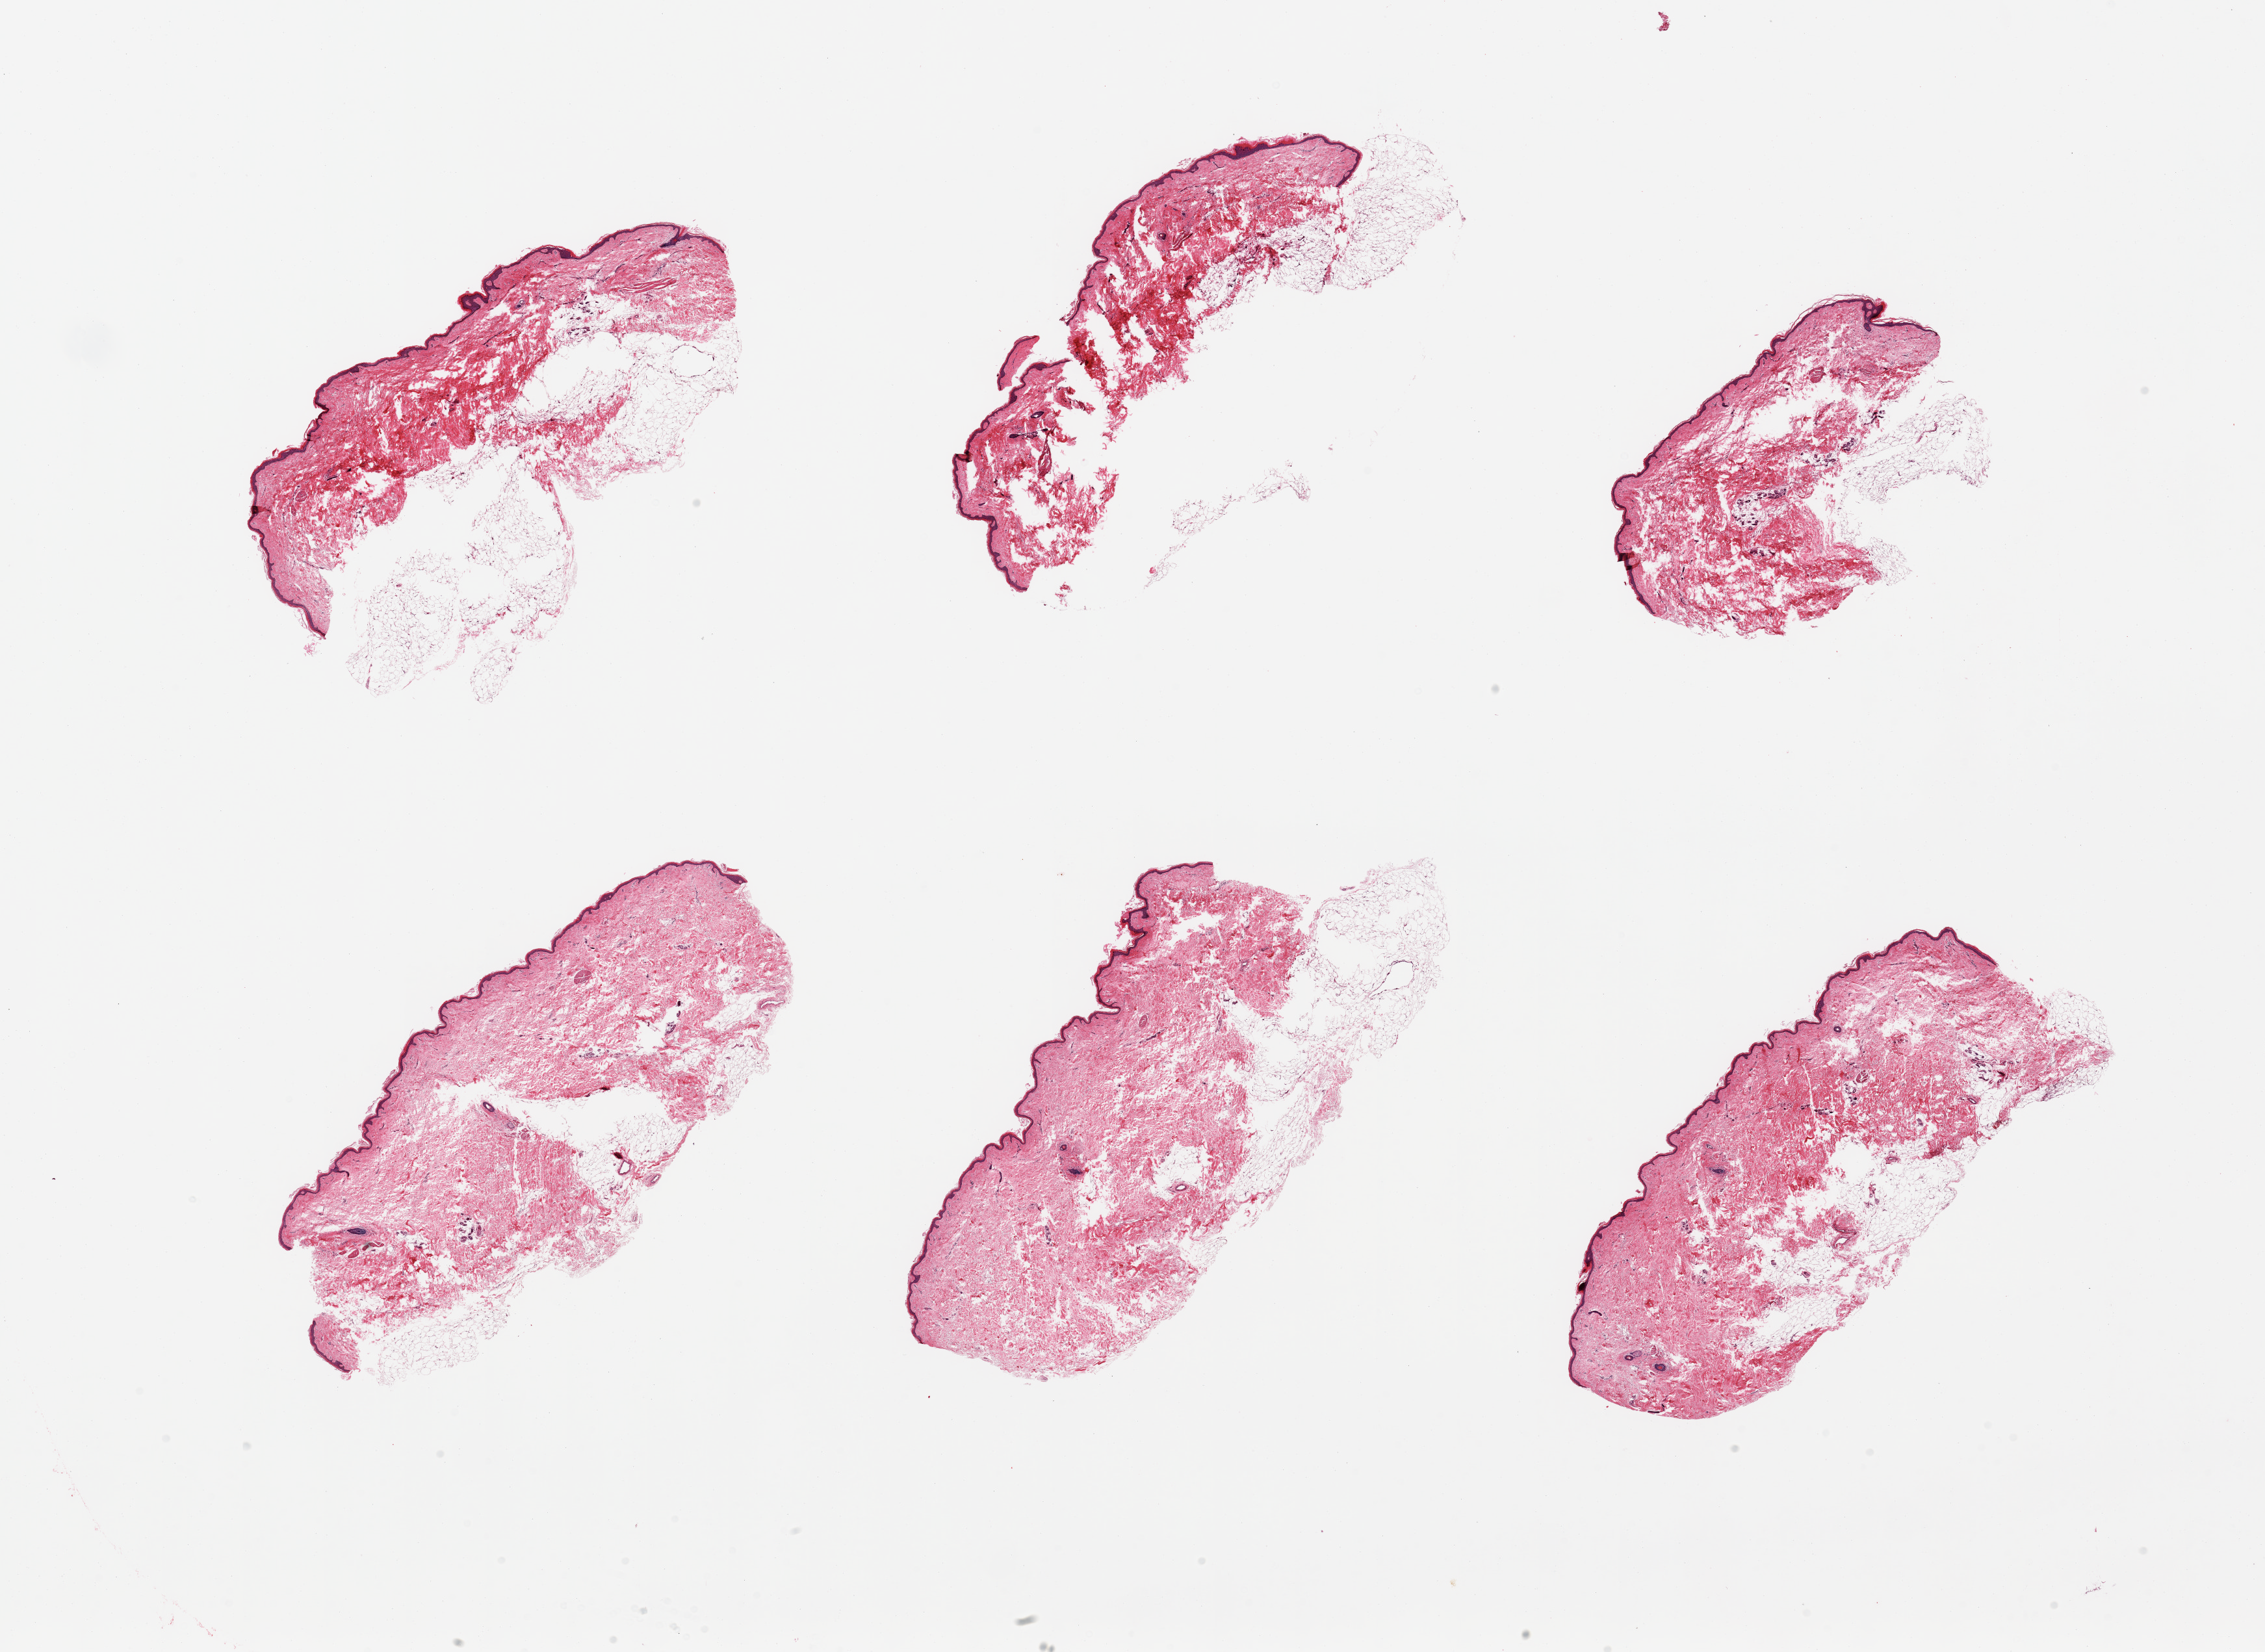
Digitized hematoxylin and eosin (H&E)-stained section, whole scanned area (about 27.6 x 20.1 mm, acquisition: 20x scan) shown as a low-resolution overview. PAXgene-fixed paraffin-embedded (PFPE) section. Sampled site (target tissue): skin of suprapubic region. Donor tissue sample. Donor: female.
Reviewer comment on this tissue sample: 6 pieces, adherent fat is ~1.5mm in some sections; squamous epithelium is ~30 microns.